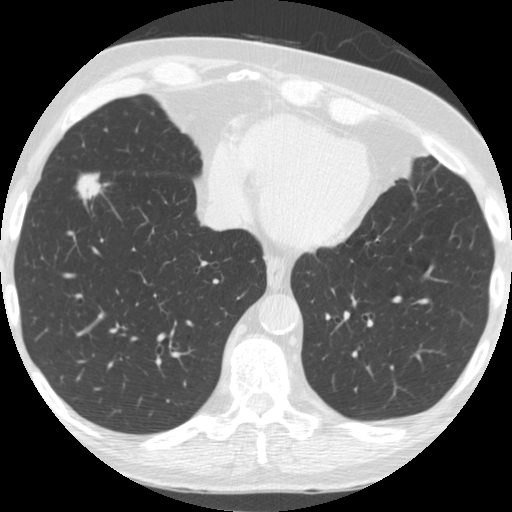
Low-dose screening chest CT, one axial slice; position 66 of 182 along the scan axis; reconstruction kernel STANDARD; 120 kVp; lung window (W 1500 / L -600 HU); 2.5 mm slice thickness; 512 × 512 image matrix.
Outlined on this slice (outlined manually by an expert reader):
- lesion 1 (tumor, lower lobe of right lung): bounding box <76,173,109,202> (left, top, right, bottom; pixels)